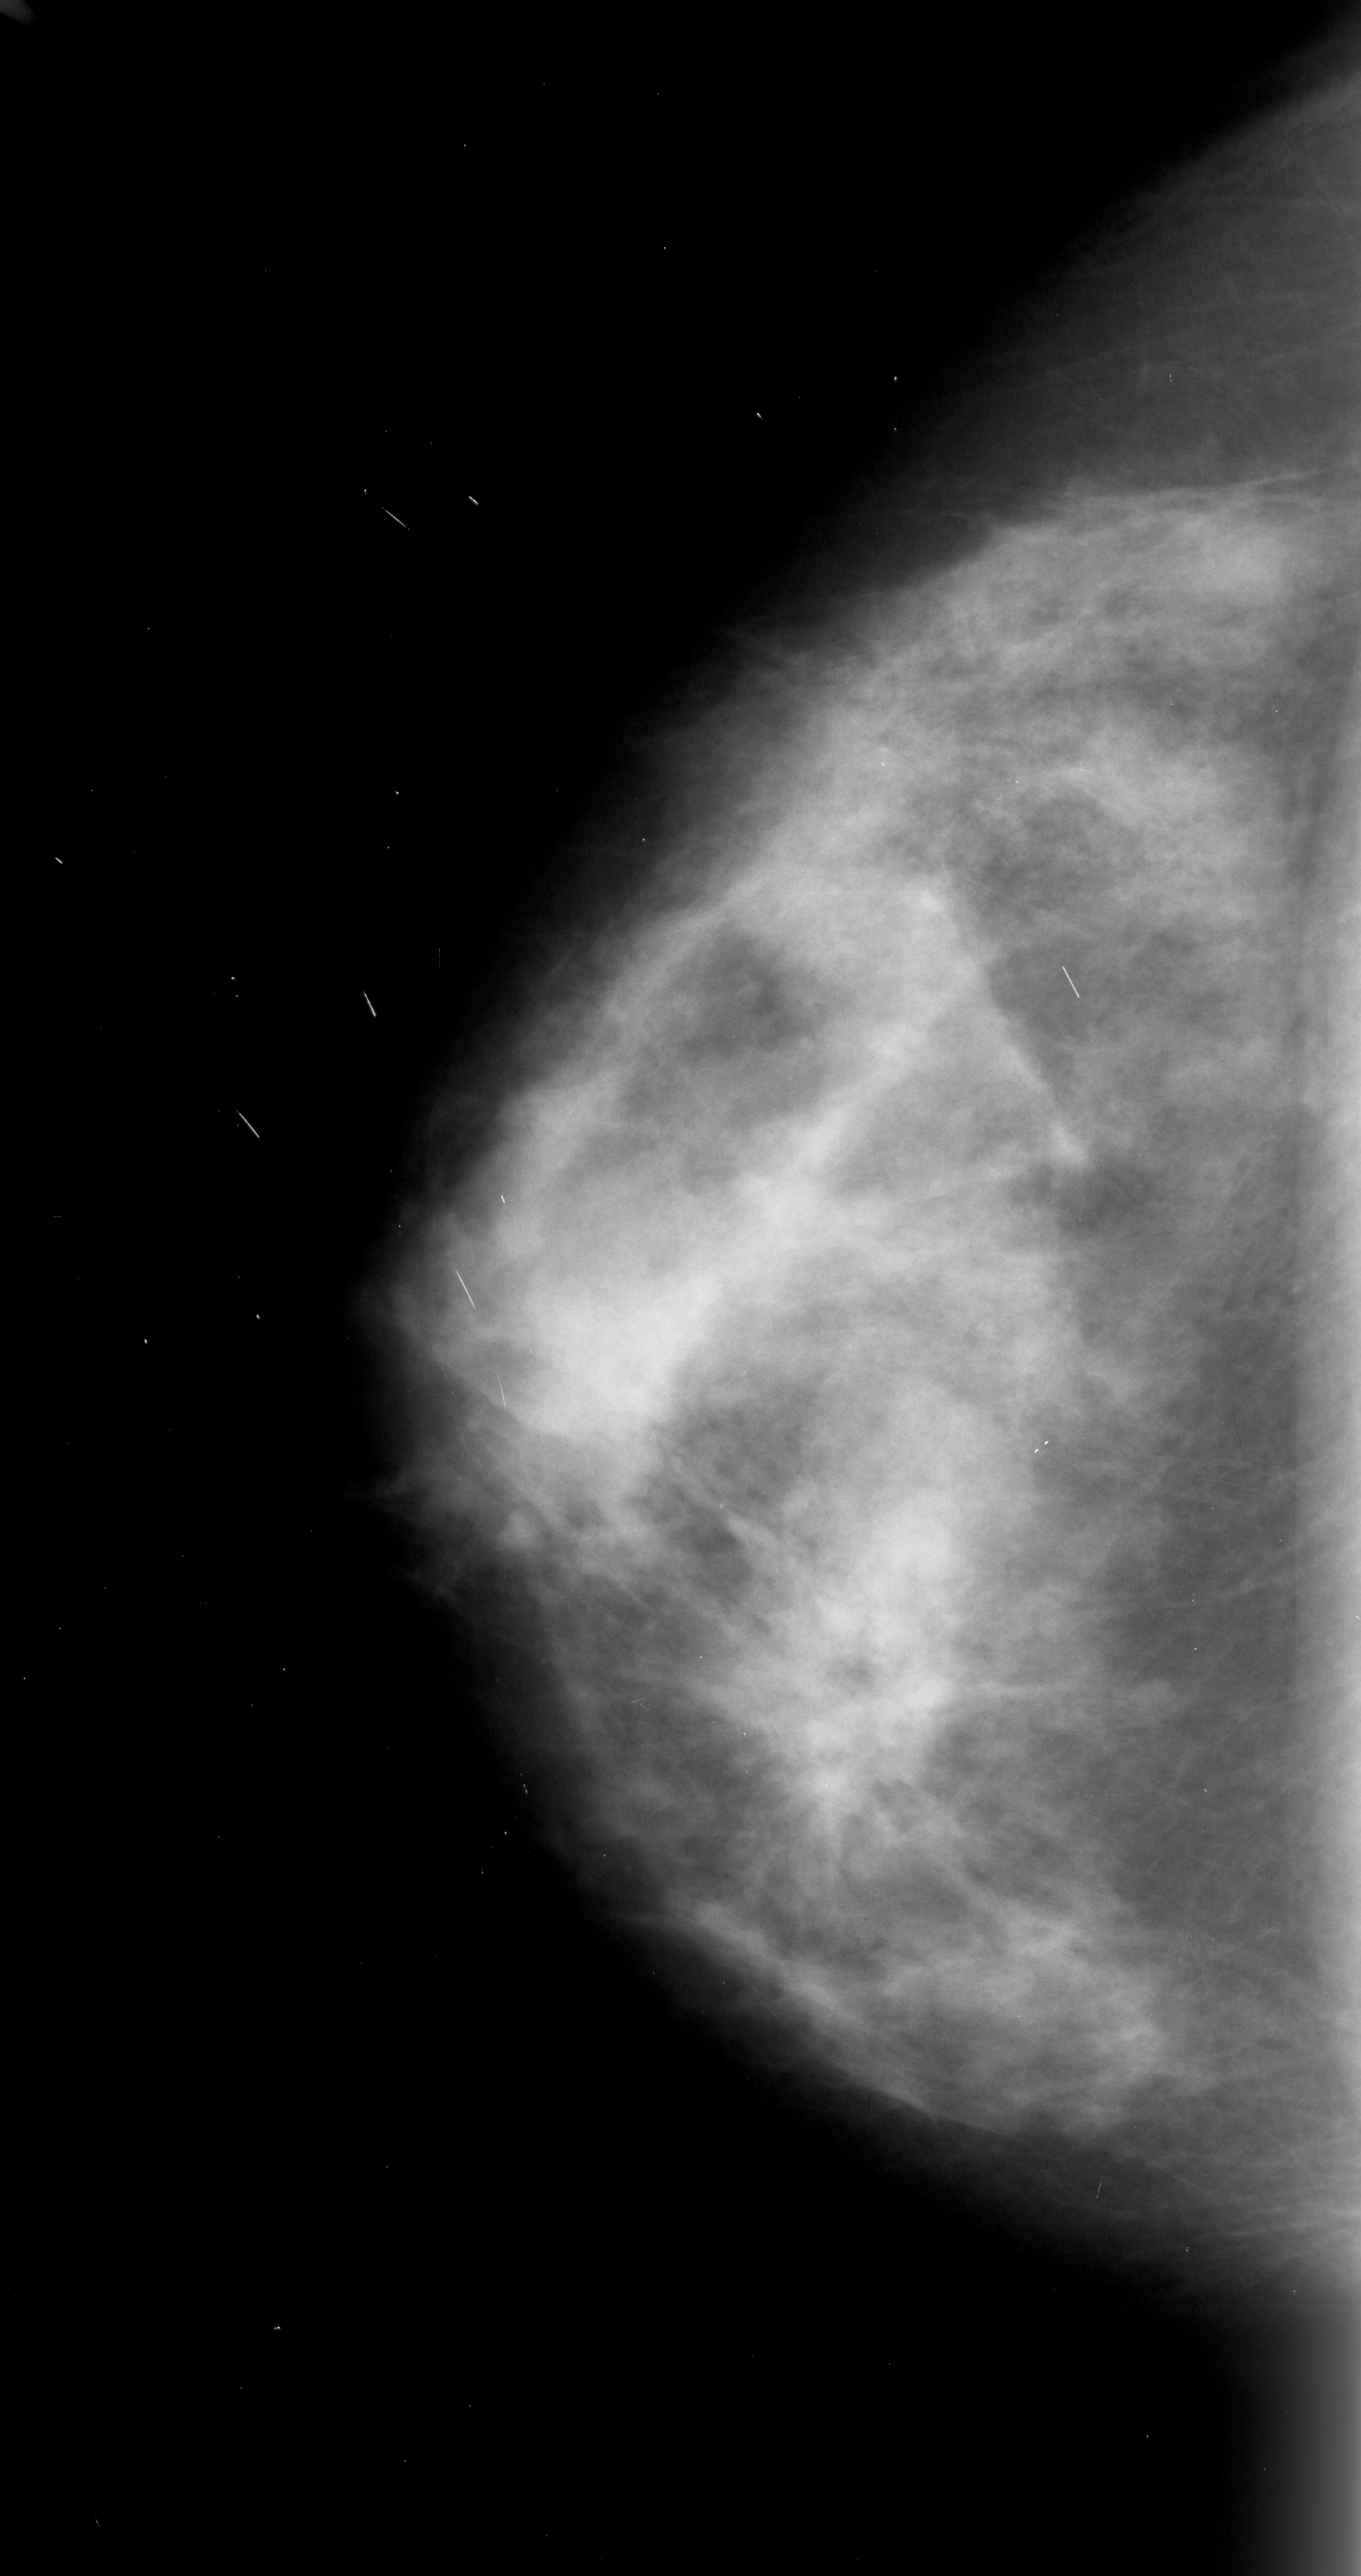
Digitized screen-film mammogram. Left breast. Craniocaudal (CC) view. Breast composition: extremely dense (BI-RADS density category 4 of 4). 1361 × 2576 image matrix.
Marked abnormalities (boxes around the expert regions of interest):
- mass, shape irregular, margins spiculated; BI-RADS assessment category 5; pathology (as recorded): malignant: bounding box [x1, y1, x2, y2] px = [680, 1541, 968, 1771]